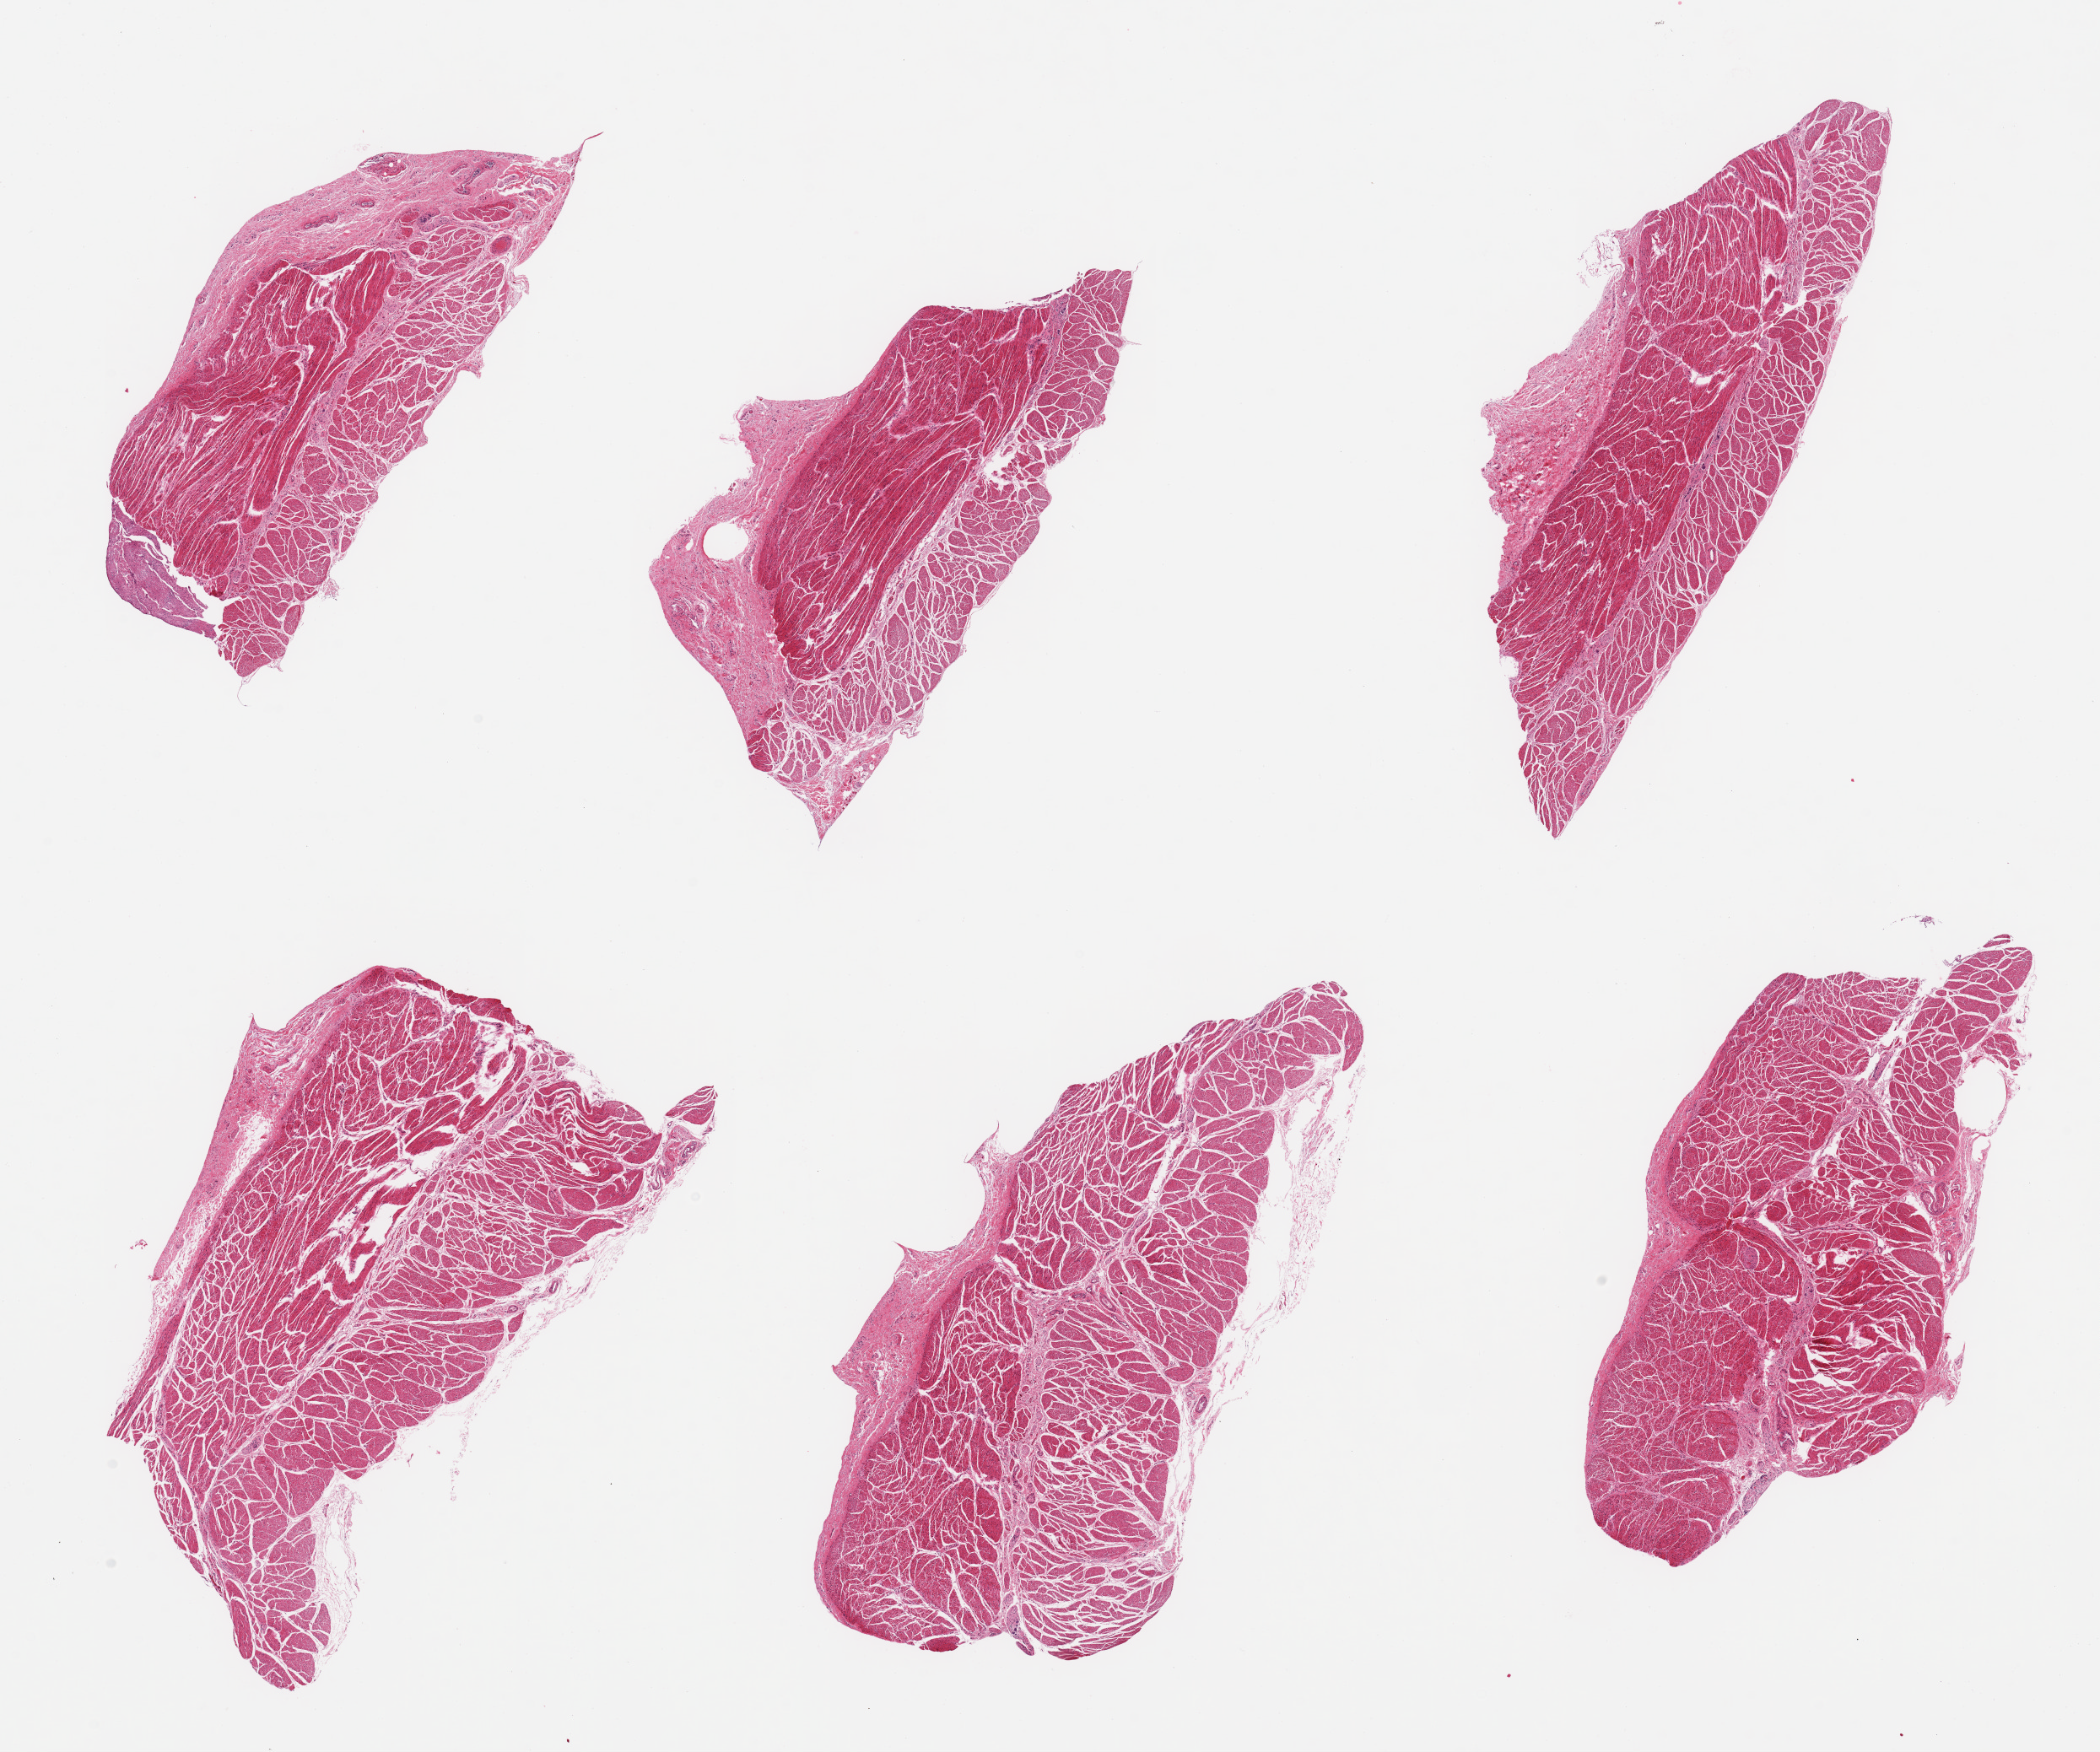
Digitized haematoxylin and eosin-stained section — shown as a low-resolution overview of the whole scanned area (about 19.7 x 16.4 mm, slide scanned at 20x). PAXgene-fixed paraffin-embedded (PFPE) section. Target tissue: gastroesophageal junction. Tissue donor sample. Donor sex: female.
Reviewer comment on this tissue sample: 6 pieces; well dissected.